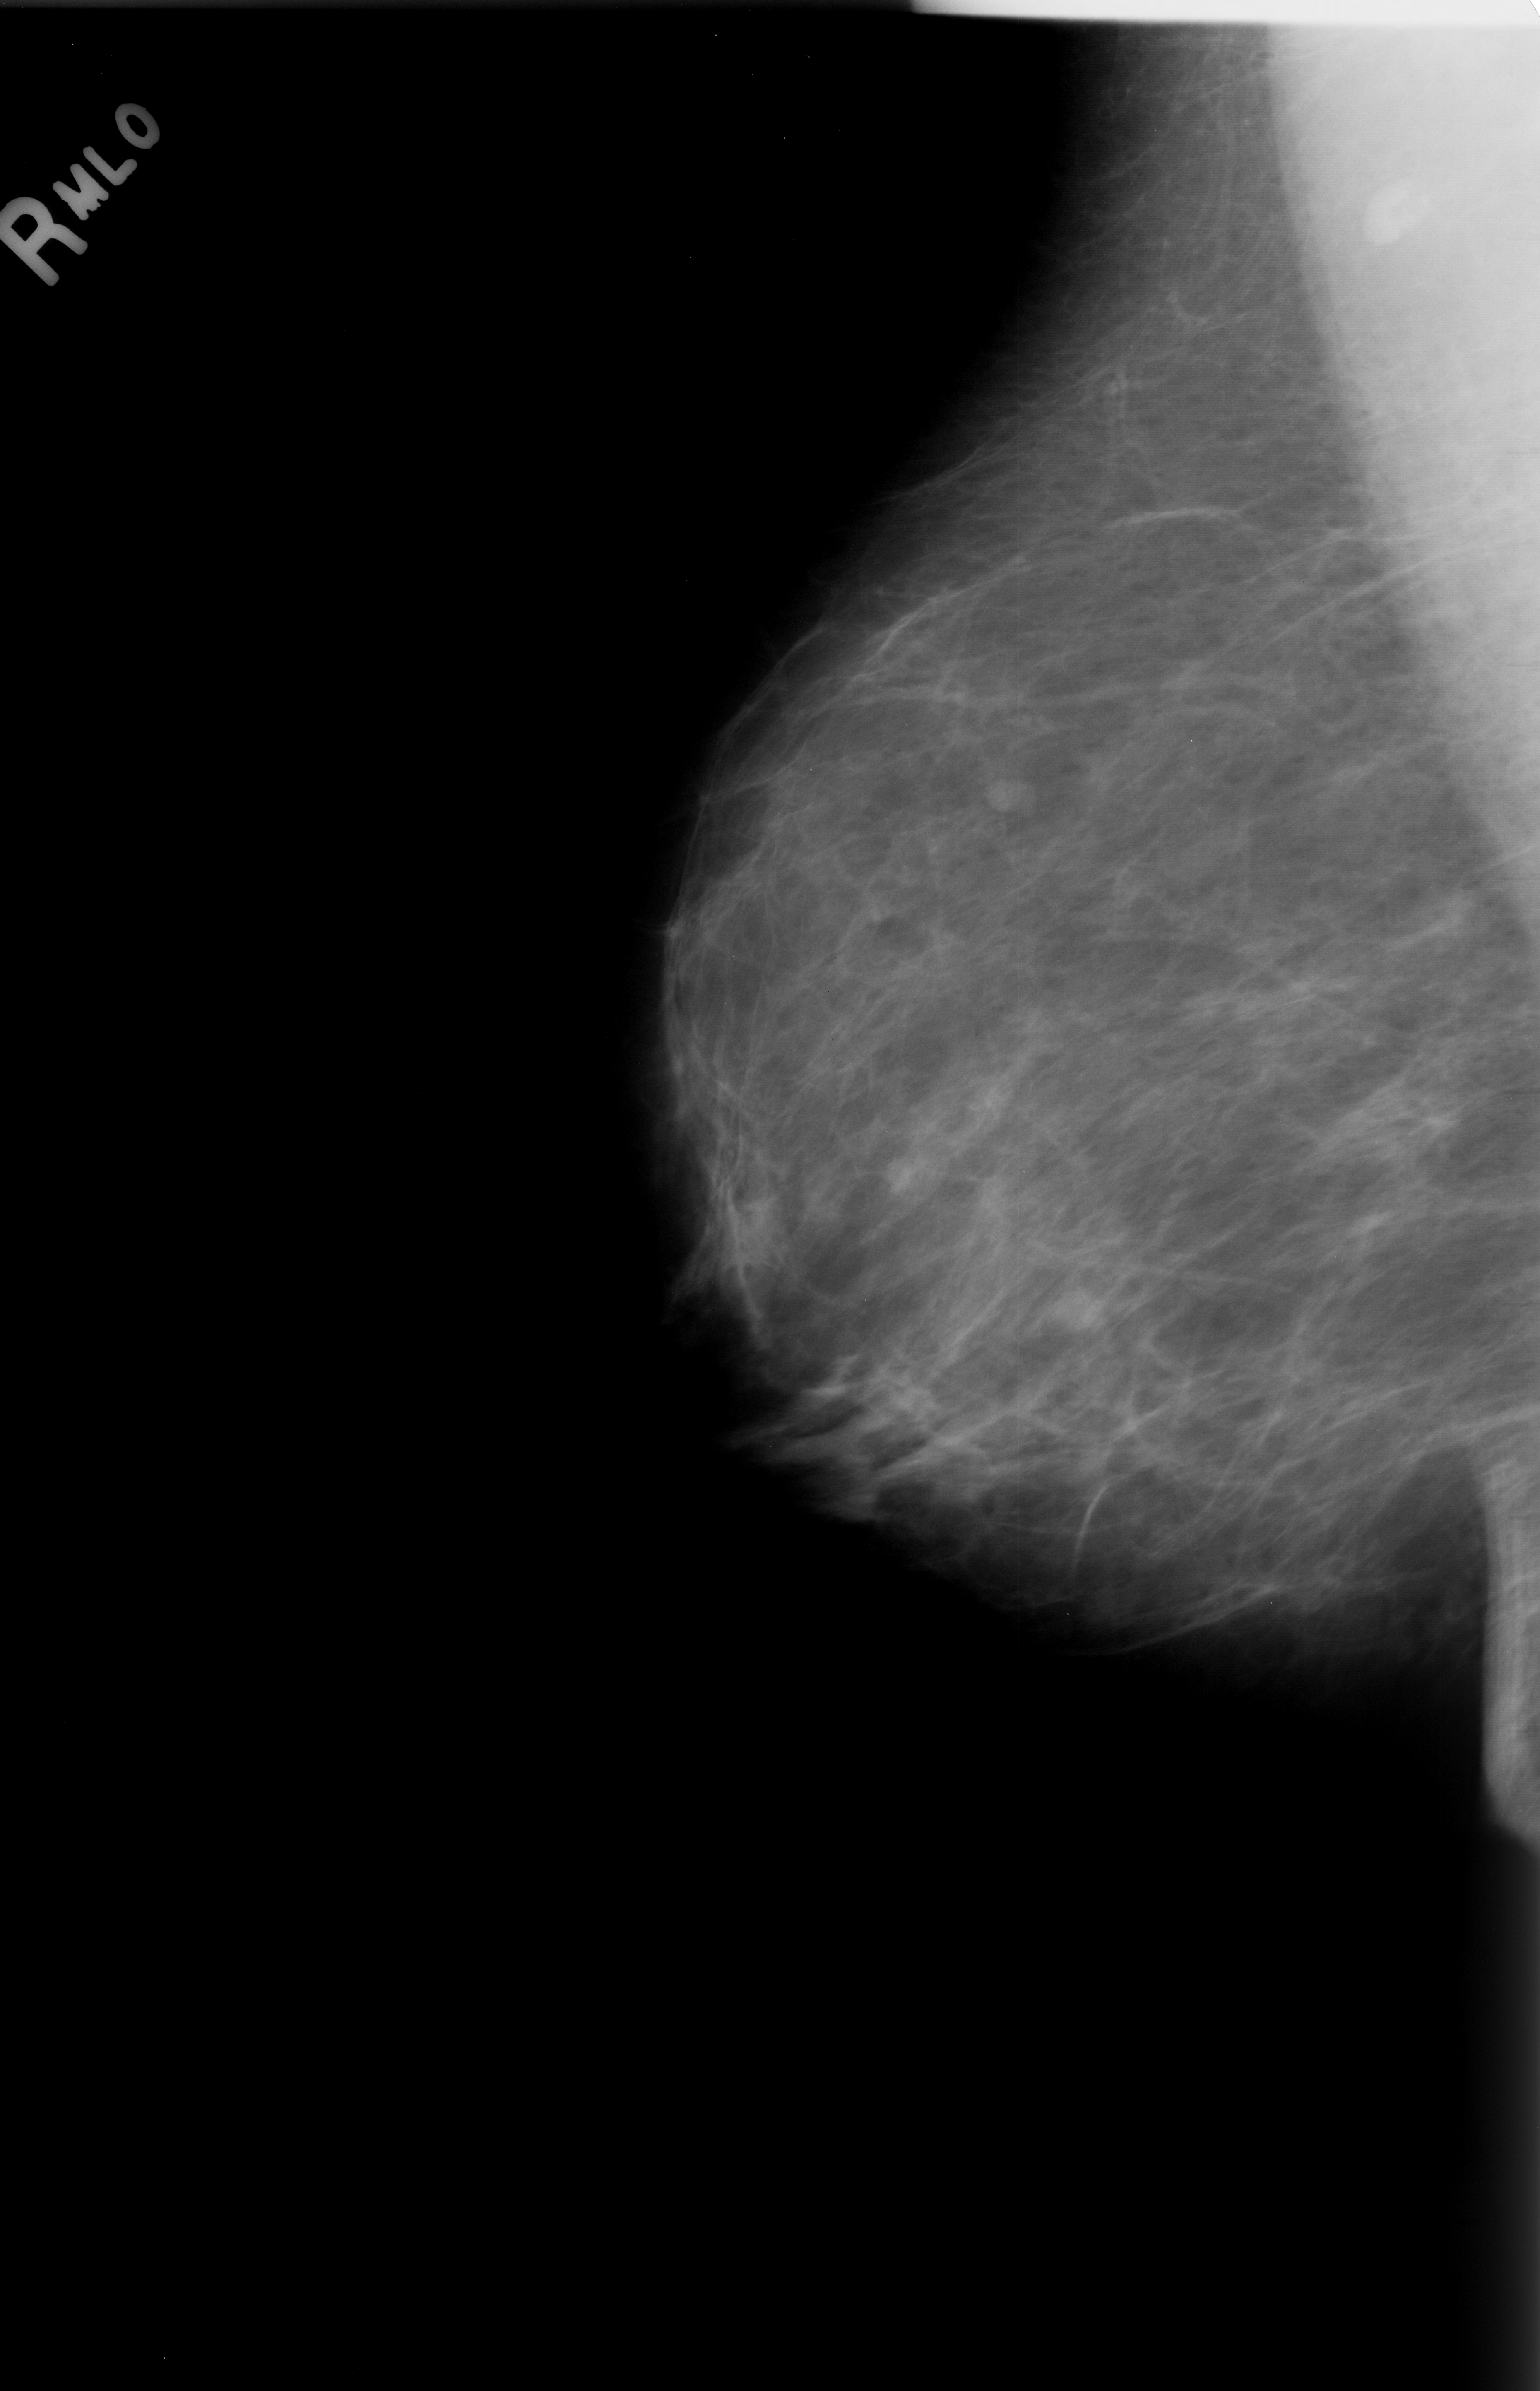
Mammogram (digitized film); right breast; mediolateral oblique (MLO) view; breast composition: almost entirely fatty (BI-RADS density category 1 of 4).
- Marked findings (only marked abnormalities are described; nothing is implied about the rest of the image): mass, shape lobulated, margins obscured; BI-RADS assessment category 3; subtlety rating 4 on a 1 (subtle) to 5 (obvious) scale; pathology result (as recorded, not read from the image): benign.